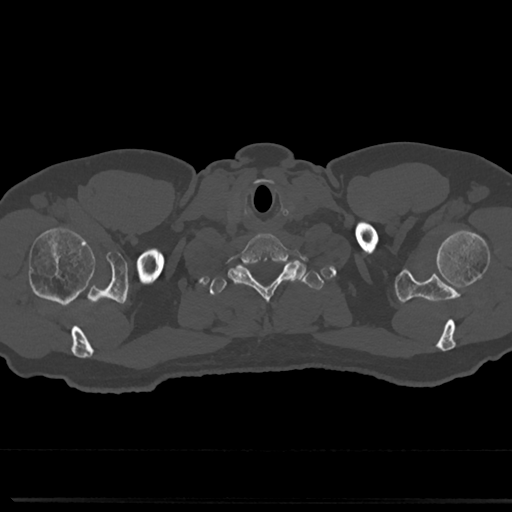
CT including the spine, one axial slice; position 695 of 817 along the scan axis; reconstruction kernel Br40s/3; 120 kVp; bone window (W 1800 / L 400 HU); 512 × 512 image matrix, field of view 355 × 355 mm. Patient: male, 61 years. Case-level facts recorded for this patient, not image findings: primary cancer: prostate.
Structures marked on this image (semi-automatically segmented with operator editing):
- T1 vertebra: box from (x=209, y=263) to (x=319, y=337) px